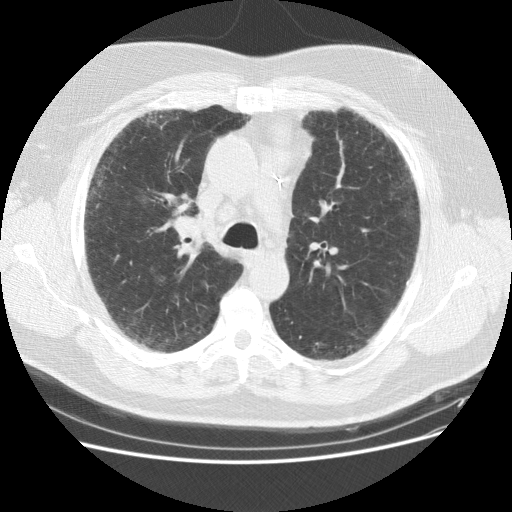
Axial slice from a low-dose chest CT screening exam, baseline screening round, lung window (W 1500 / L -600 HU), standard (soft-tissue) reconstruction kernel (STANDARD), 120 kVp, 512 × 512 image matrix, field of view 378 × 378 mm. Male, age 59 years at enrolment.
- Expert reader's lesion annotation, box from (x=165, y=205) to (x=206, y=245) px.
- The screening reader recorded 2 non-calcified nodules or masses ≥4 mm on this exam (right middle lobe, right lower lobe); which of them this box marks is not recorded.
- Lung cancer was diagnosed 338 days after this screen: adenocarcinoma, NOS, right upper lobe, right middle lobe, moderately differentiated (G2), stage IA (AJCC 6th edition), 13 mm at pathology.